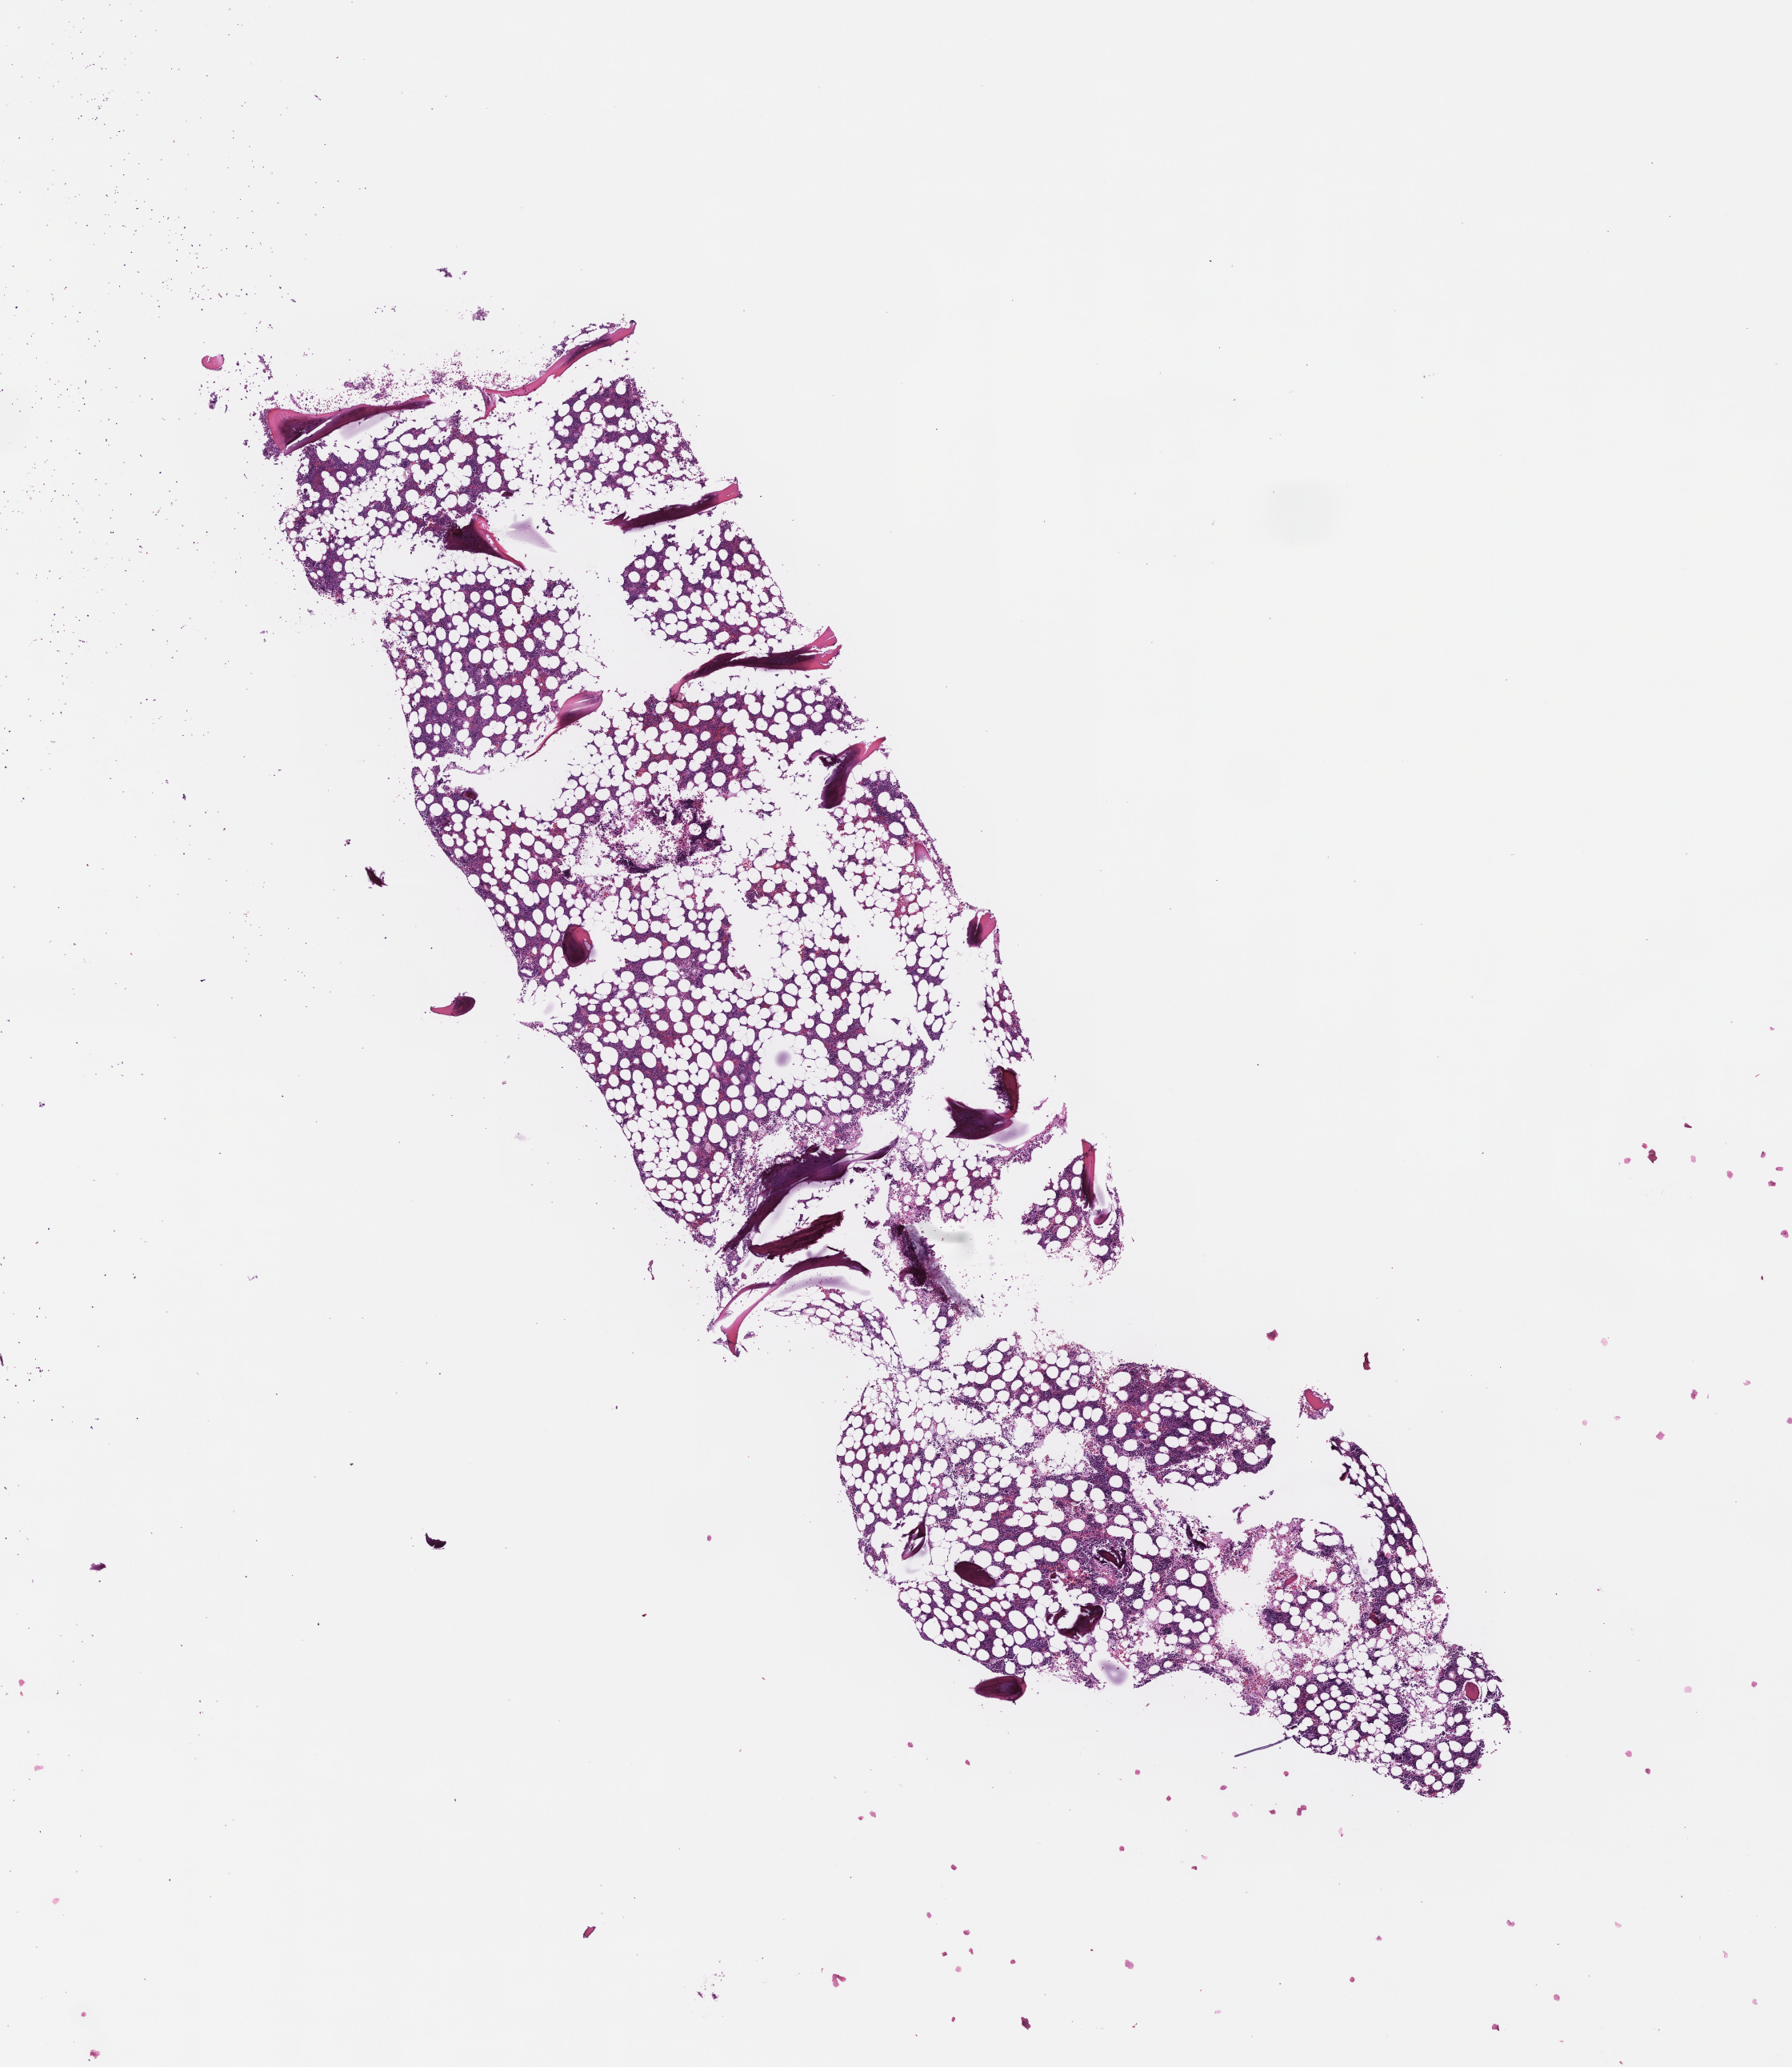
Haematoxylin and eosin whole-slide image — low-resolution overview of the scanned area, about 9.0 x 10.4 mm. FFPE section. Site: bone marrow. Archival tissue. Male patient.
This section: primary tumour tissue. Diagnosis: Plasma Cell Myeloma.